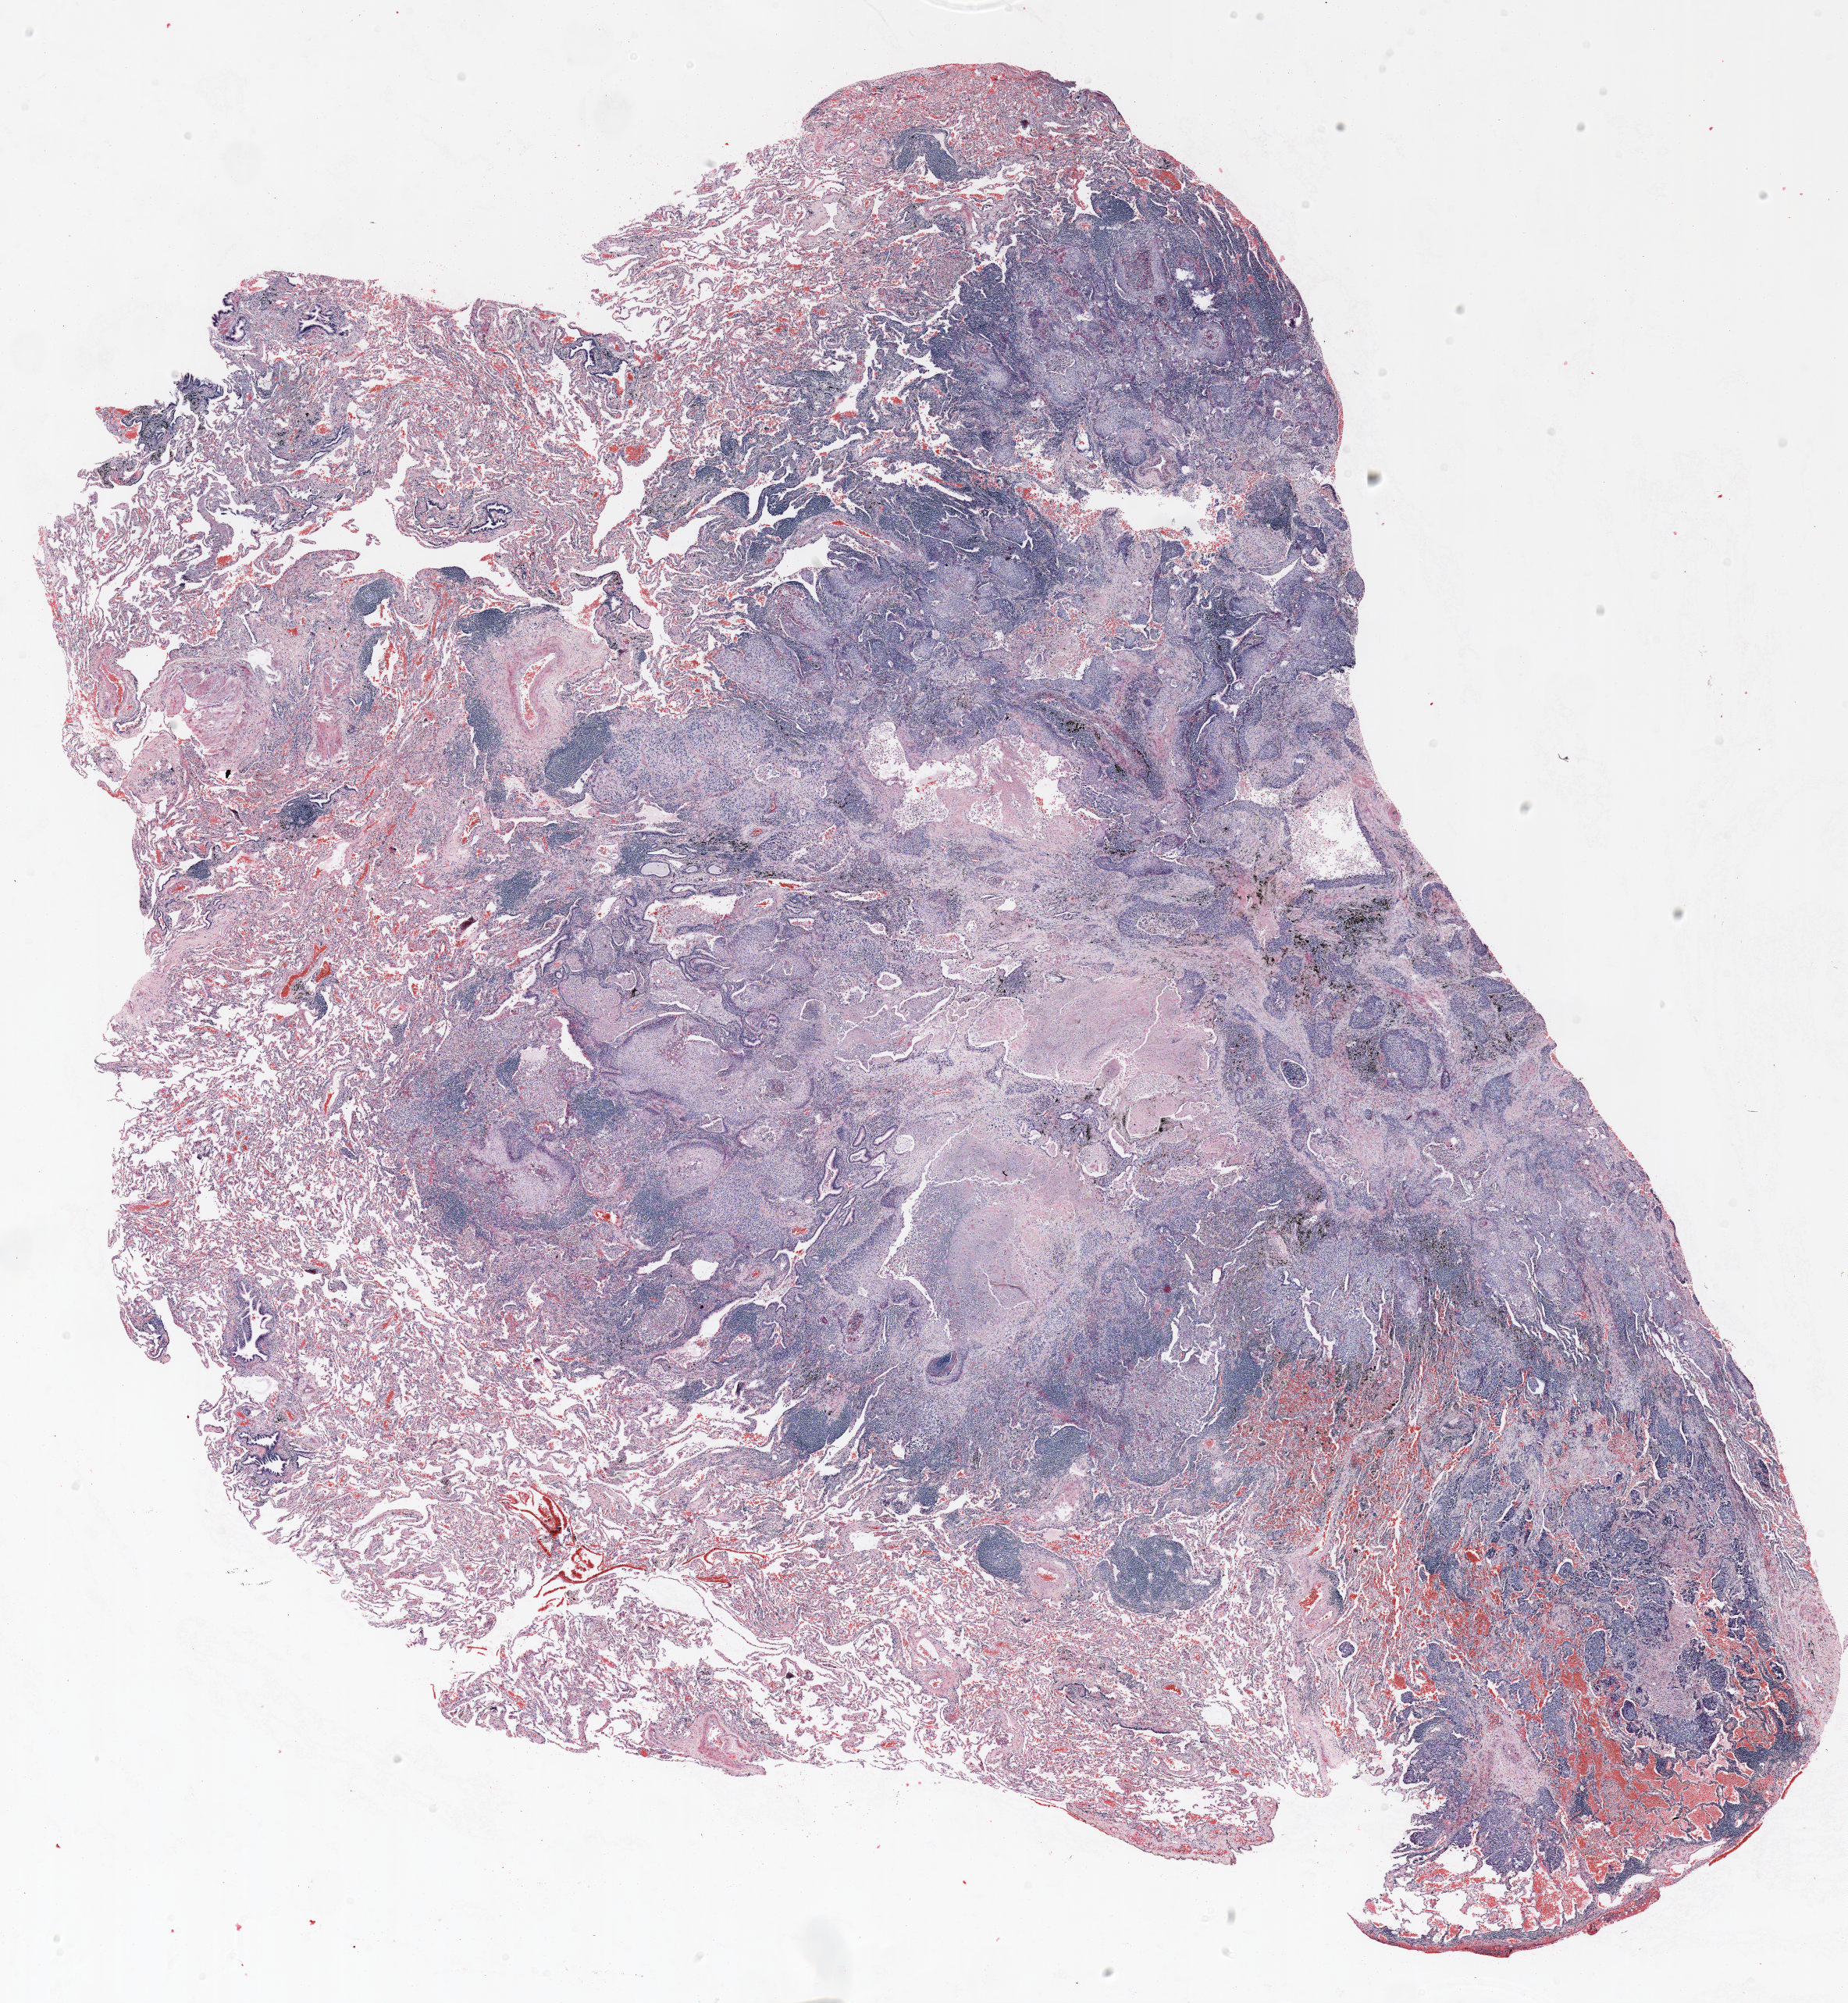
Whole-slide histology image, H&E-stained — a low-resolution overview of the entire scanned area, about 19.0 x 20.6 mm (from a 20x scan). FFPE section. Lung tissue. Male patient, aged 59 at enrolment. Grade: moderately differentiated (G2).
* participant's lung-cancer diagnosis: Squamous cell carcinoma, NOS
* stage (AJCC 6th edition): IA
* primary tumour location (clinical record): left upper lobe
* tumour size (pathology): 27 mm